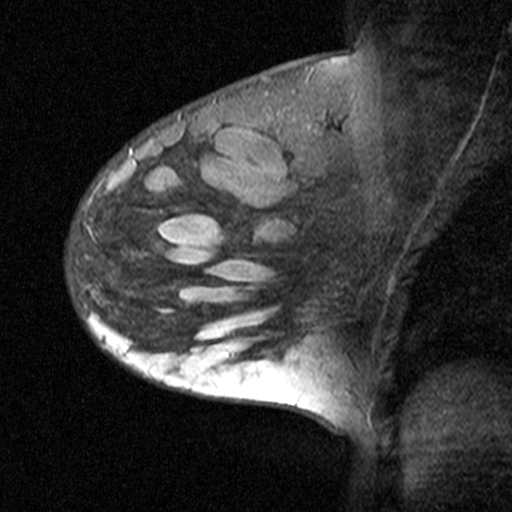
Breast MRI (dynamic contrast-enhanced), one sagittal slice. Position 29 of 44 along the scan axis. Dynamic contrast-enhanced study with each time point stored as its own series, time point 2 of 3 at this slice position (early post-contrast, ordered by acquisition time). 1.5 T. TE 4.5 ms, TR 11 ms. 3 mm slice thickness. 512 × 512 image matrix, field of view 200 × 200 mm. Patient: female, 27 years. Case-level facts recorded for this patient, not image findings: setting: breast cancer imaged before/during neoadjuvant chemotherapy; receptor status: HR-positive, HER2-negative.
Structures marked on this image (semi-automatic segmentation, software-assisted and operator-edited):
- analysis volume of interest (the breast-tissue region the enhancement analysis was run in; not a lesion): bounding box (x1, y1, x2, y2) in pixels: (67, 162, 163, 271)
- tumour enhancement mask (voxels above the 90 % enhancement threshold inside the analysis volume of interest): (160, 231, 162, 234)